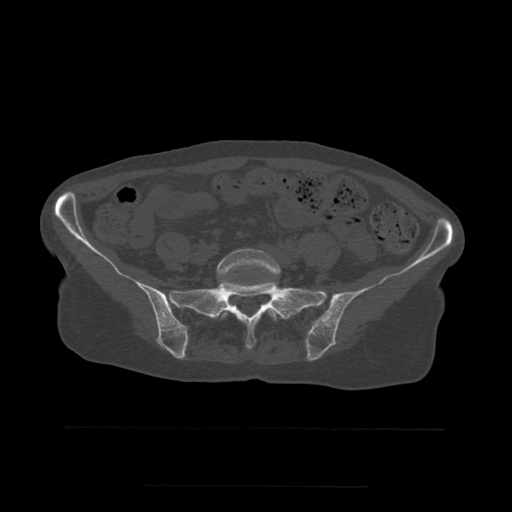
CT including the spine, one axial slice; position 133 of 544 along the scan axis; bone window (W 1800 / L 400 HU); 1.25 mm slice thickness; 512 × 512 image matrix, field of view 350 × 350 mm. Patient age 58 years. Case-level facts recorded for this patient, not image findings: primary cancer: lung.
Annotated regions visible in this slice (semi-automatically segmented with operator editing):
- L5 vertebra: bounding box <217,249,281,322> (left, top, right, bottom; pixels)